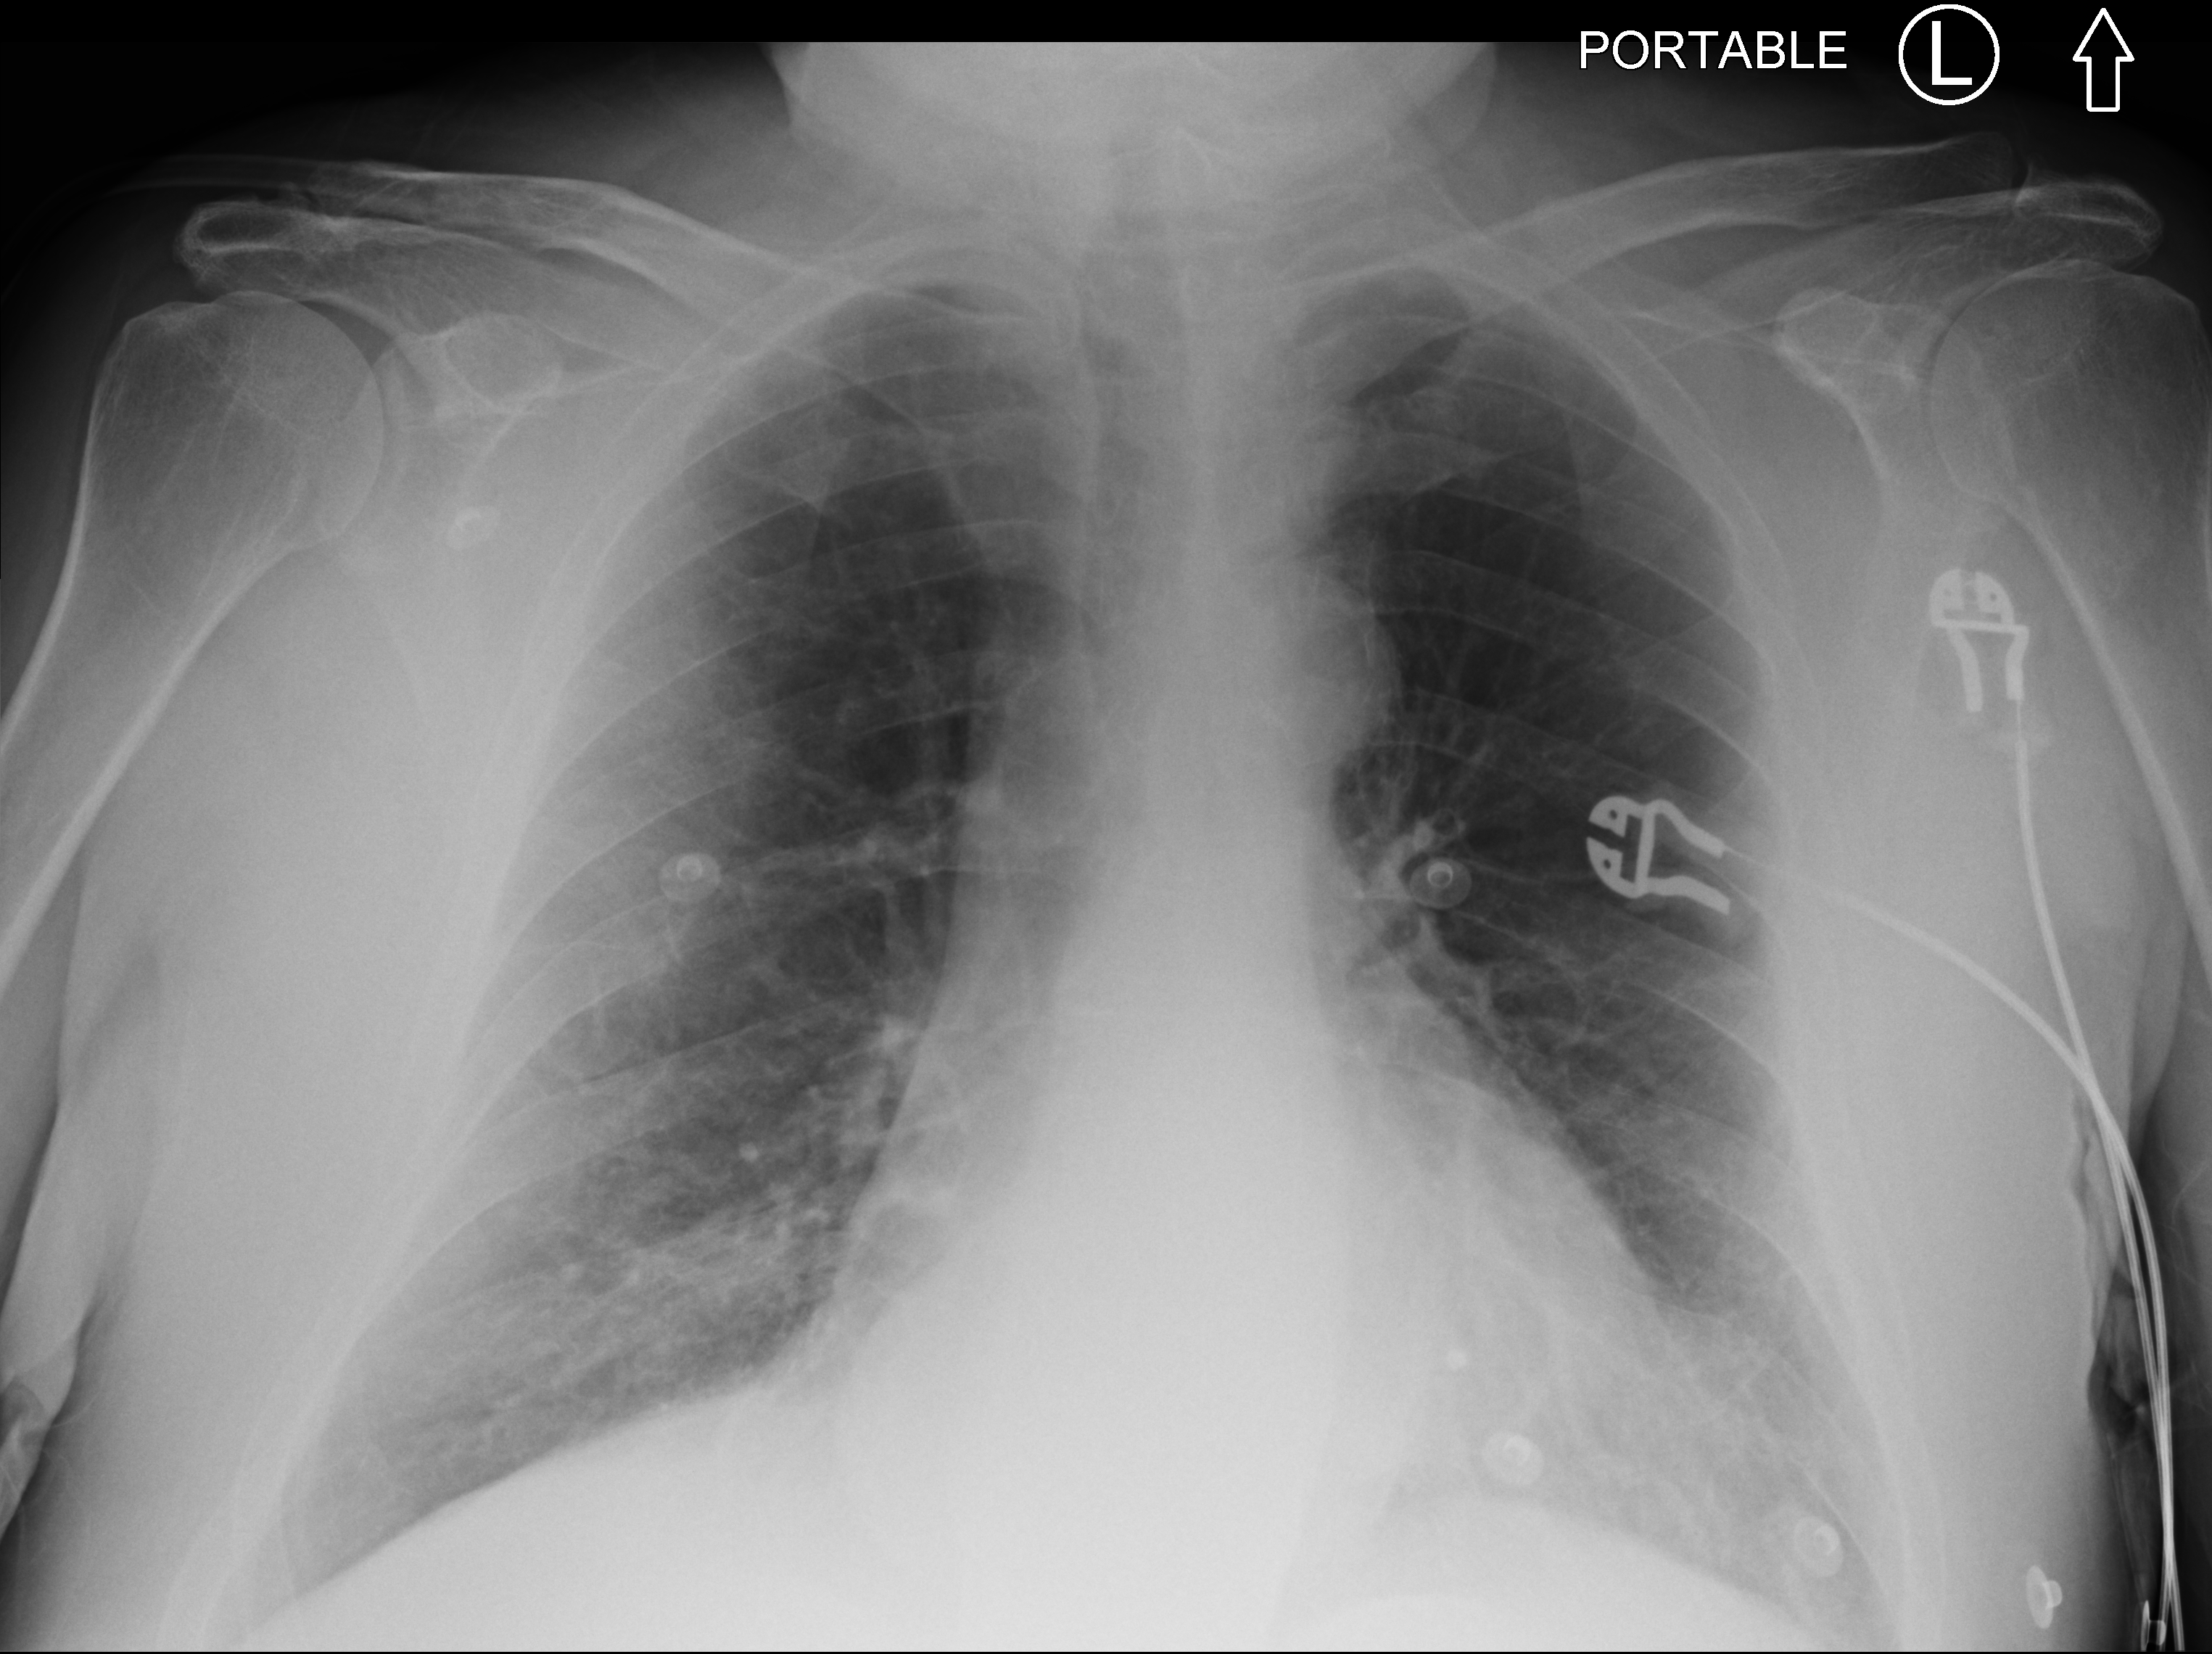
Bedside chest radiograph (computed radiography); anteroposterior (AP) projection. Male patient hospitalised with COVID-19, age 75–90 years.
Admission-level facts for this patient (not findings on this image; timing relative to this image not recorded): smoking status (admission record): never; other chronic lung disease (admission record): no.